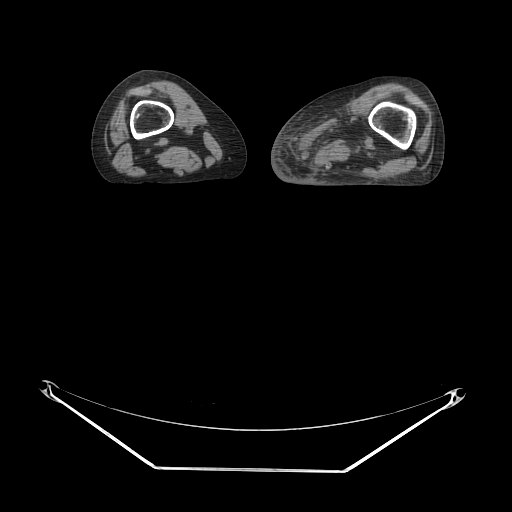
CT of an extremity soft-tissue mass (from a PET/CT study), one axial slice. Slice 2 of 91 in the series (ordered by position). Soft-tissue window (W 400 / L 40 HU). 3.75 mm slice thickness. 512 × 512 image matrix. Female patient. From the clinical record (not read from this slice): histological type: pleomorphic leiomyosarcoma; grade: high; site of the primary tumour: left thigh.
Outlined on this slice (expert contour drawn on MRI and transferred to this co-registered scan by the dataset authors):
- gross tumour volume including surrounding oedema: bounding box (x1, y1, x2, y2) in pixels: (308, 103, 378, 172)